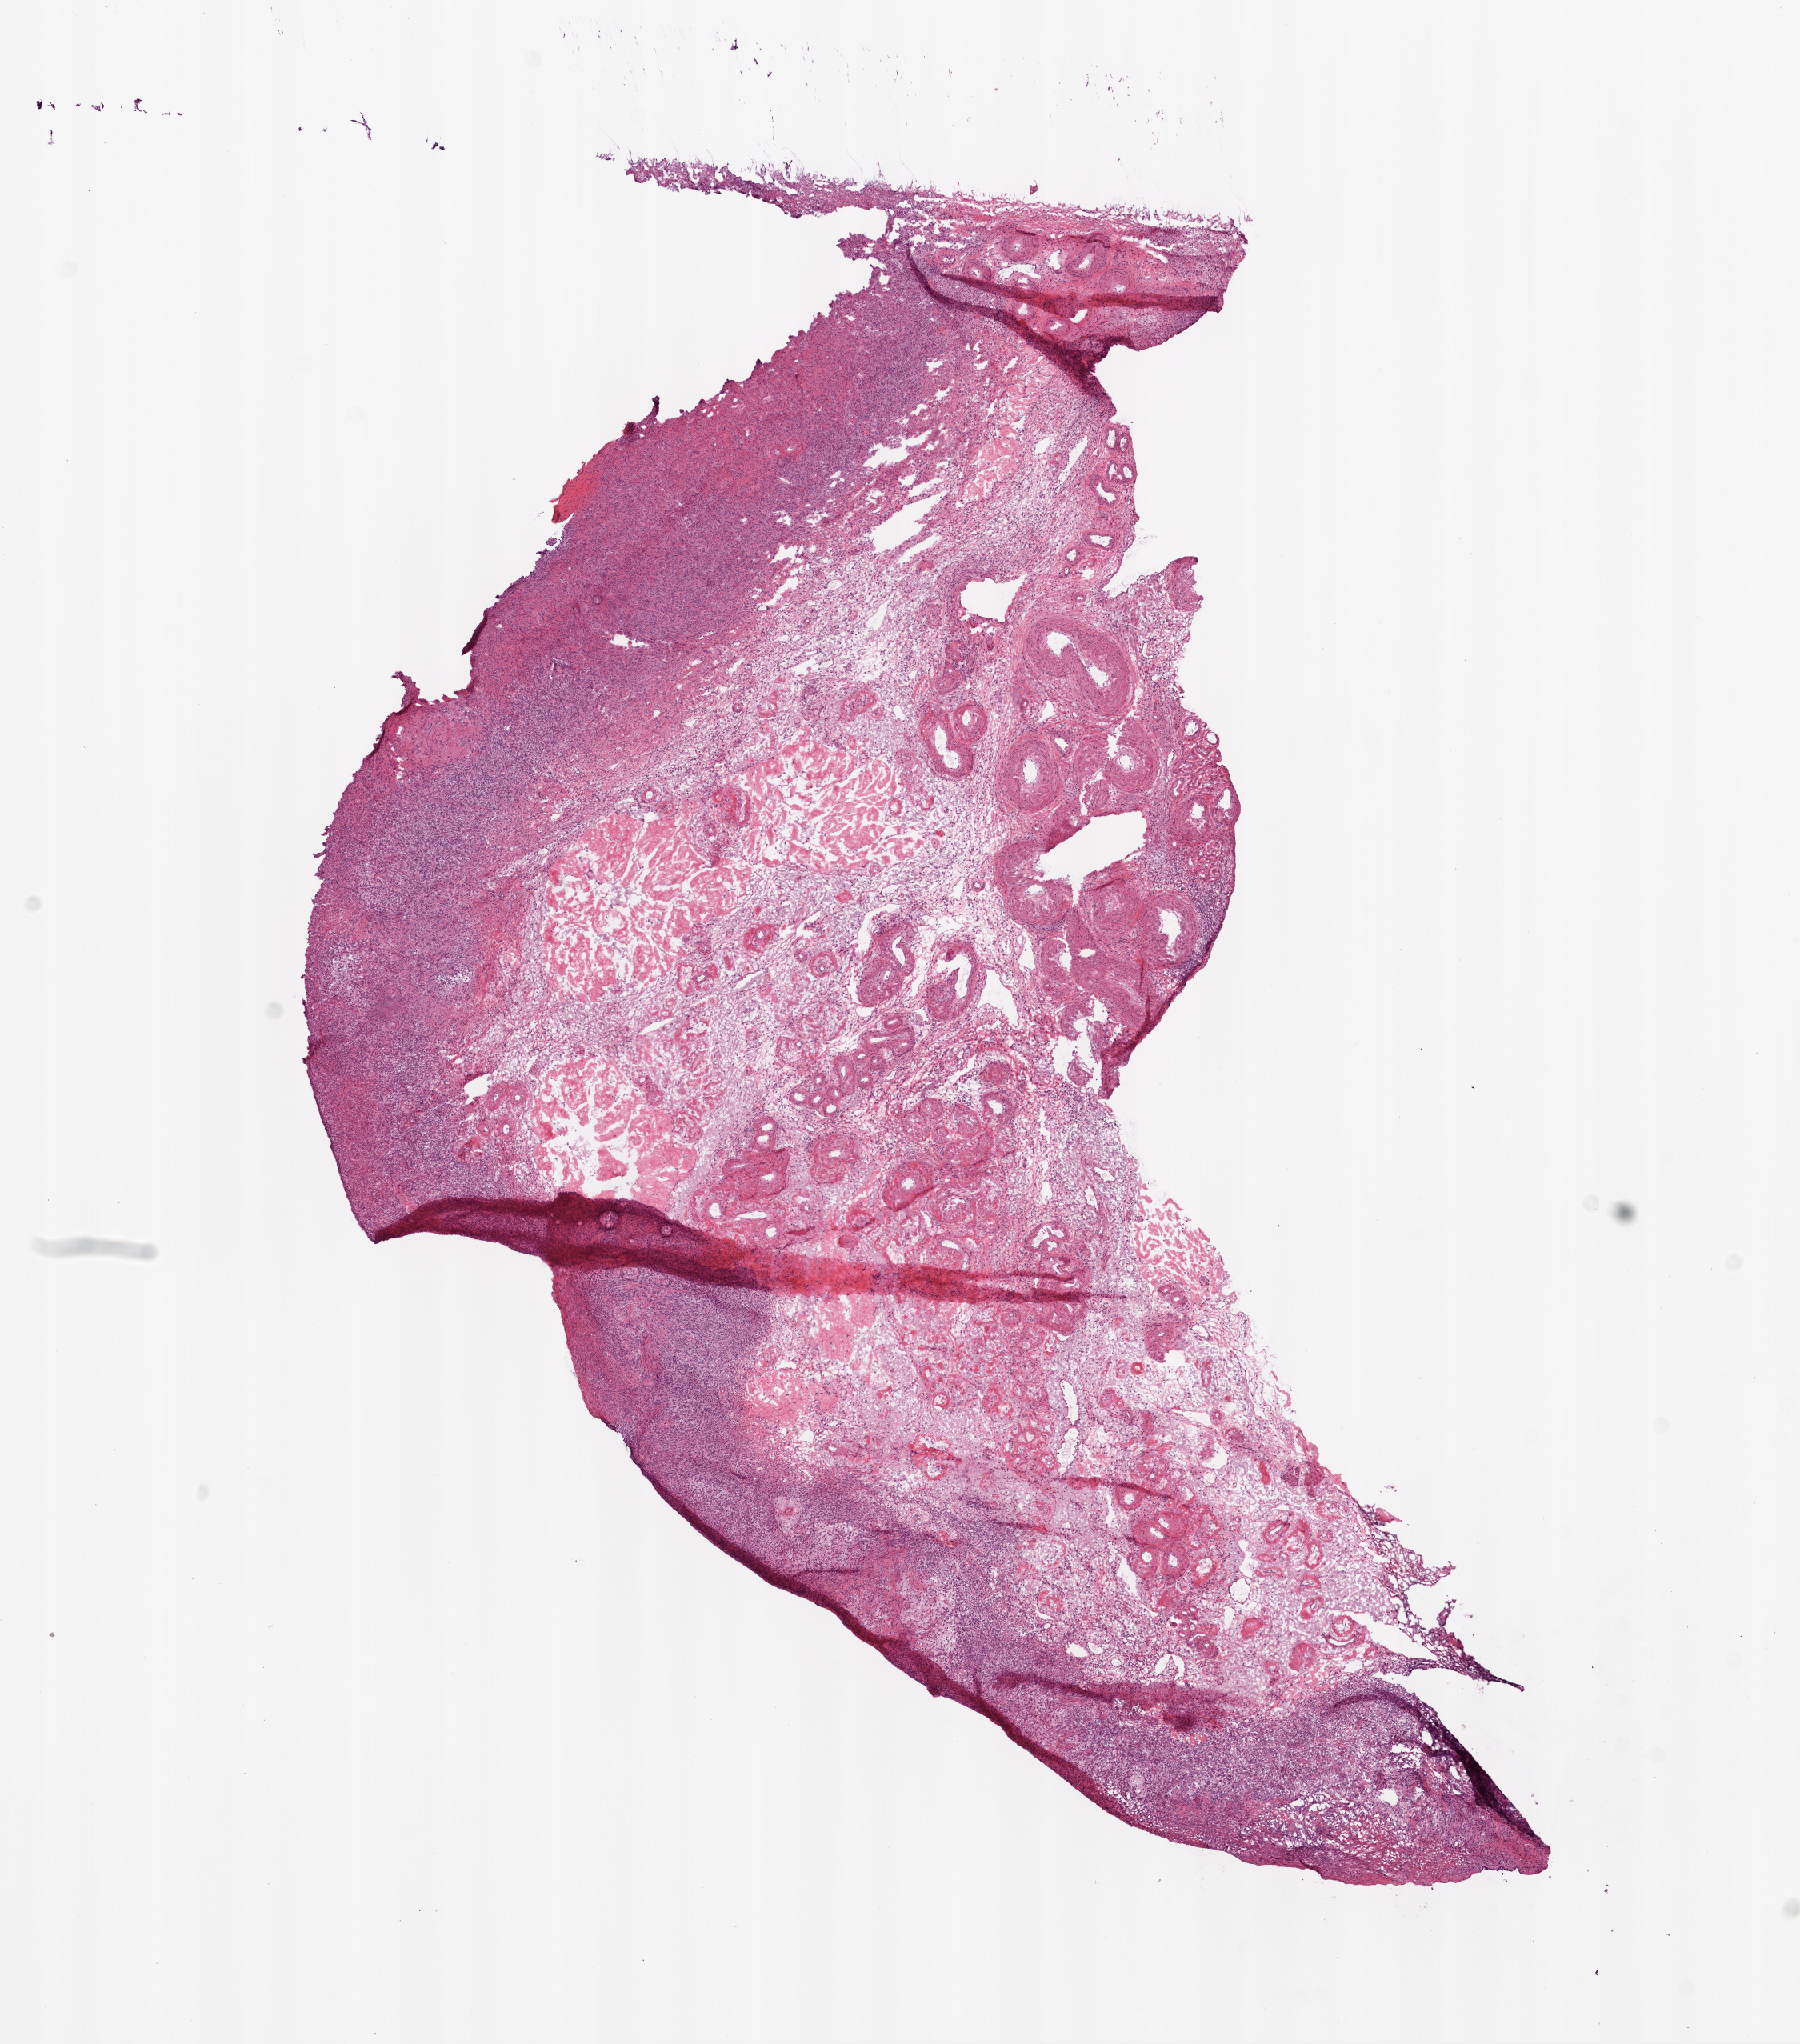
H&E-stained whole-slide image — low-resolution overview of the scanned area, about 9.0 x 10.3 mm (acquisition: 20x scan); frozen section; solid tissue normal (non-tumour tissue) sample from the ovary. Female patient; age at initial diagnosis 73 years.
- this section: solid tissue normal sample (biorepository sample class)
- patient diagnosis: Serous cystadenocarcinoma, NOS